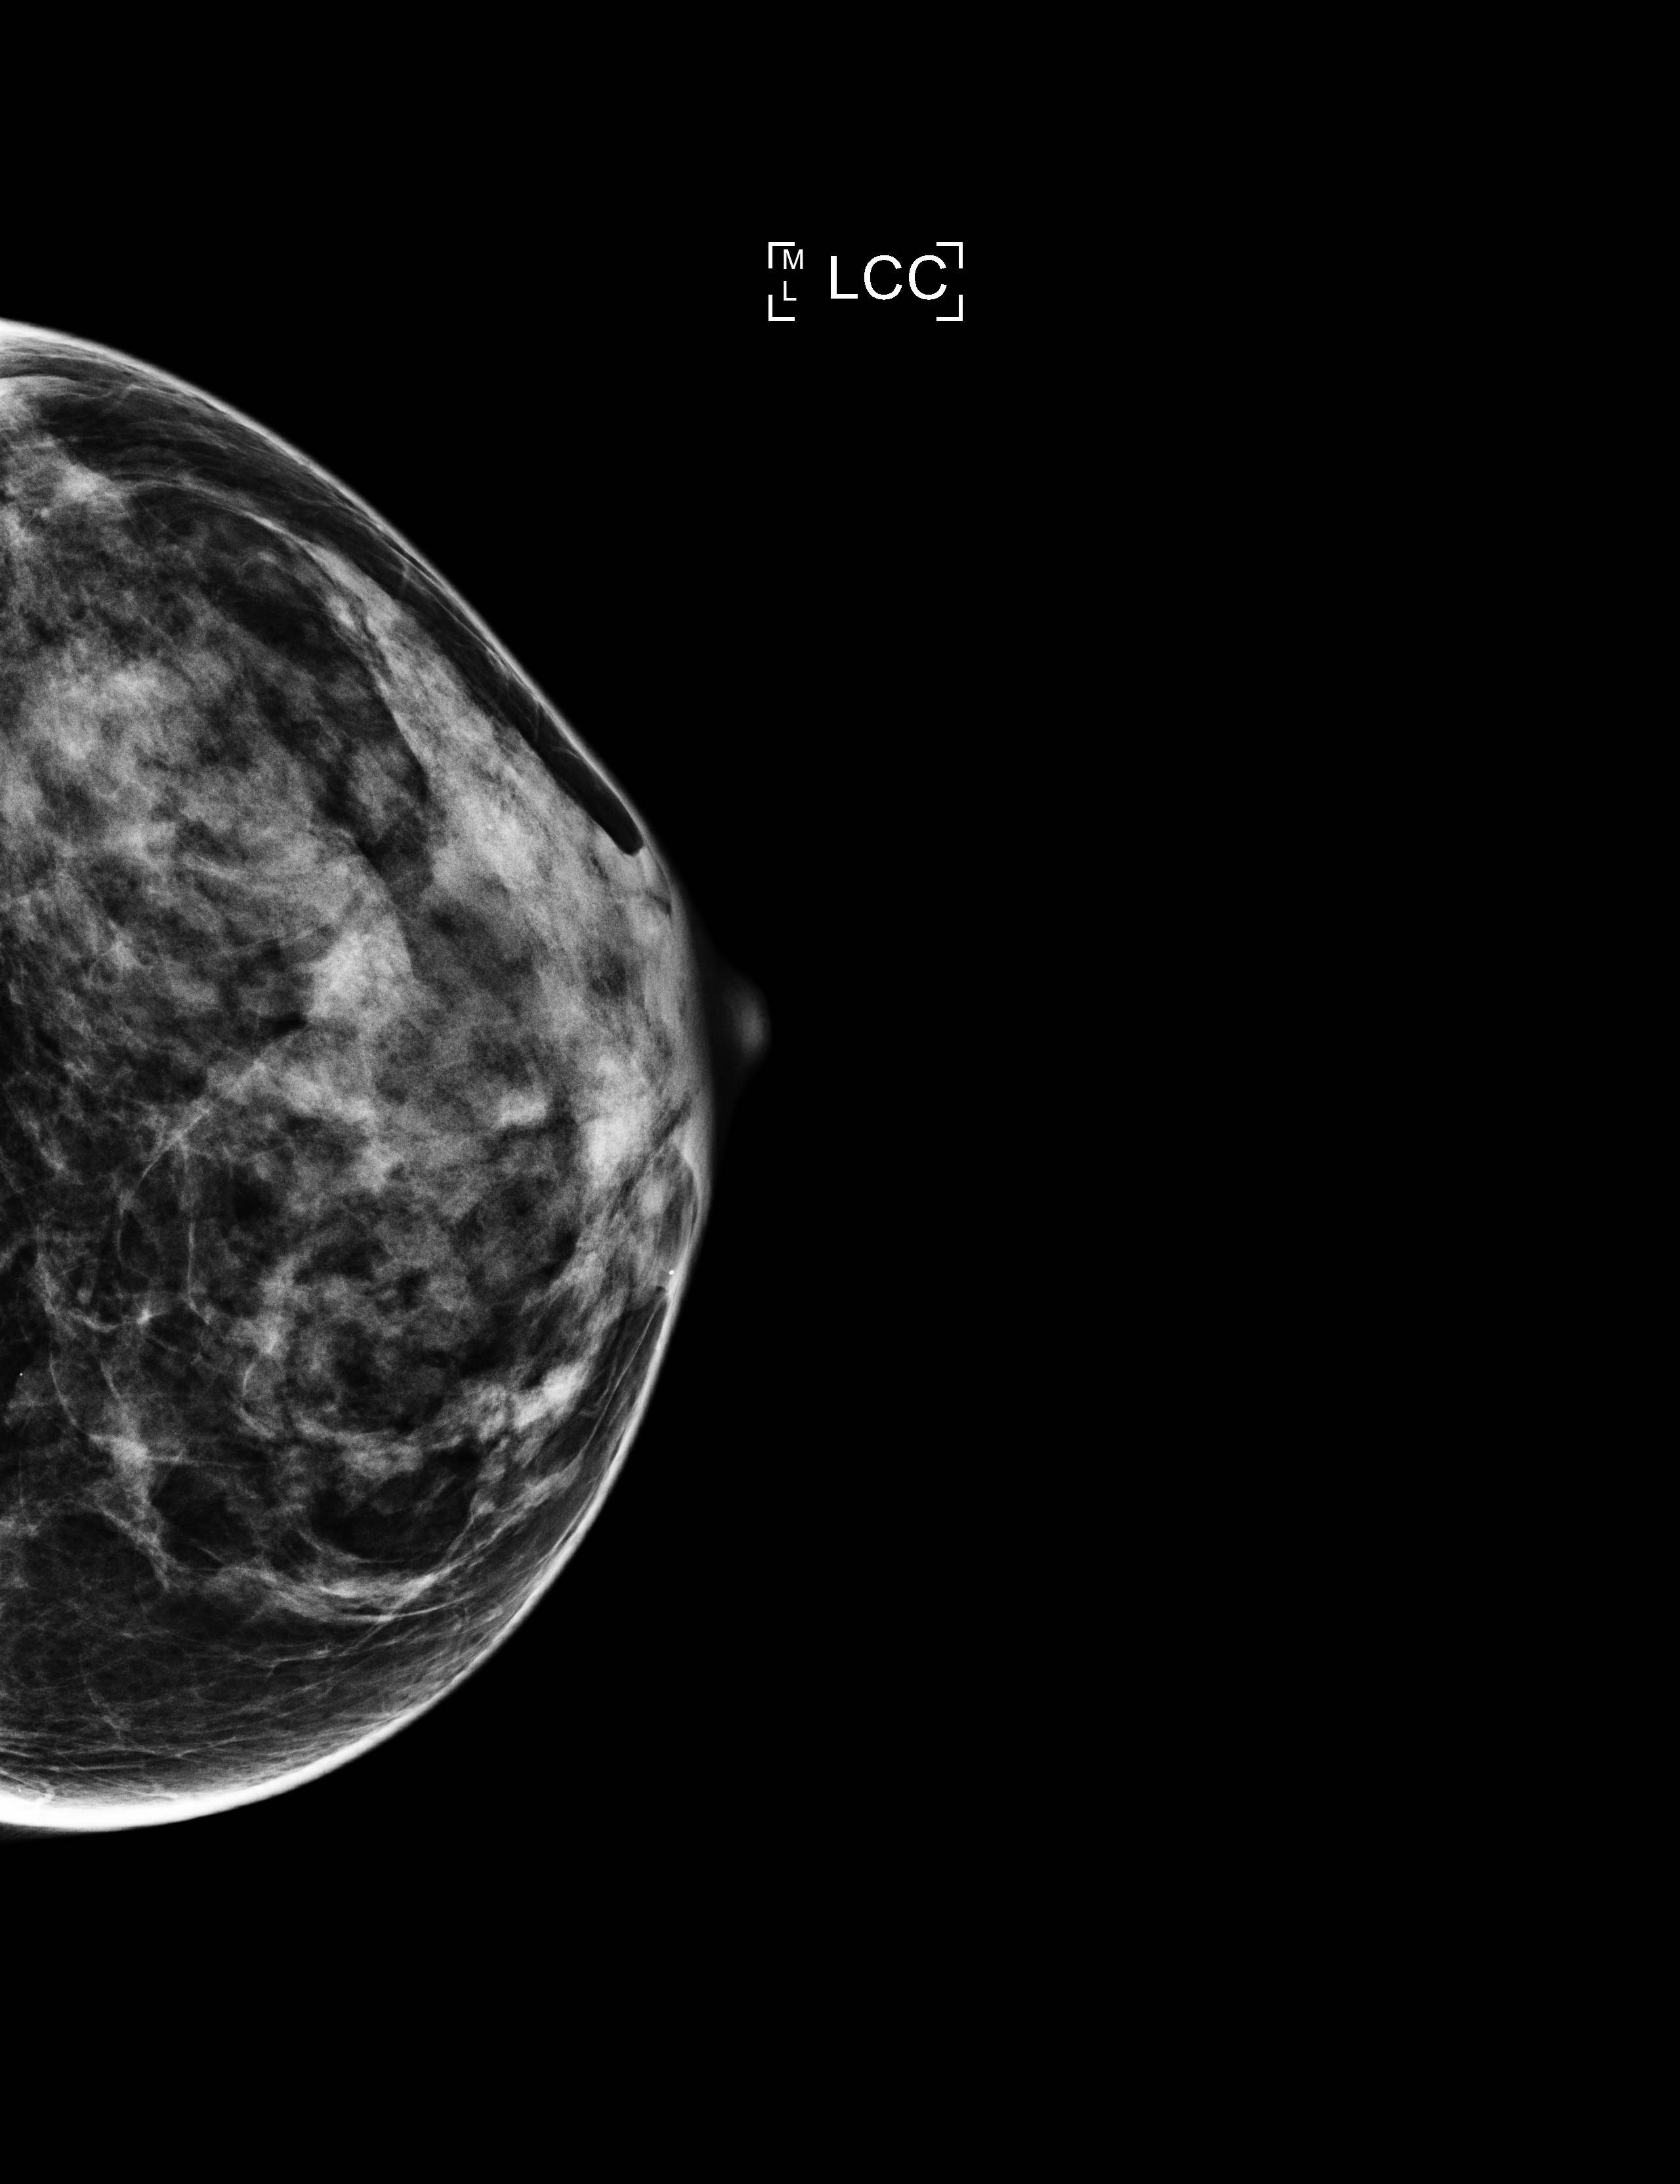
Digital mammogram (FFDM); left breast; cranio-caudal projection; annual screening mammography examination; compressed breast thickness 41 mm. Patient aged 52 years (female).
- breast density at the screening exam (both breasts): heterogeneously dense (BI-RADS density category c)
- final BI-RADS assessment for this screening round (tomosynthesis exam, both breasts): category 2
- recall: no recall after this screen